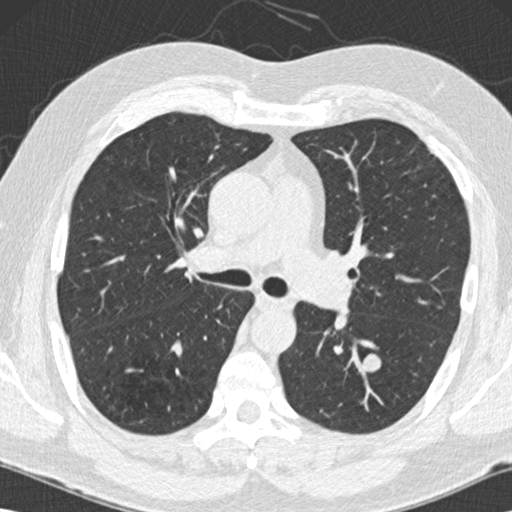
Low-dose screening chest CT, one axial slice. Slice 89 of 152 in the series (ordered by position). Reconstruction kernel B30f. Lung window (W 1500 / L -600 HU). 2 mm slice thickness. 512 × 512 image matrix, field of view 350 × 350 mm.
Annotated regions visible in this slice (outlined manually by an expert reader):
- lesion 2 (nodule, lower lobe of left lung): bounding box <362,354,381,372> (left, top, right, bottom; pixels)